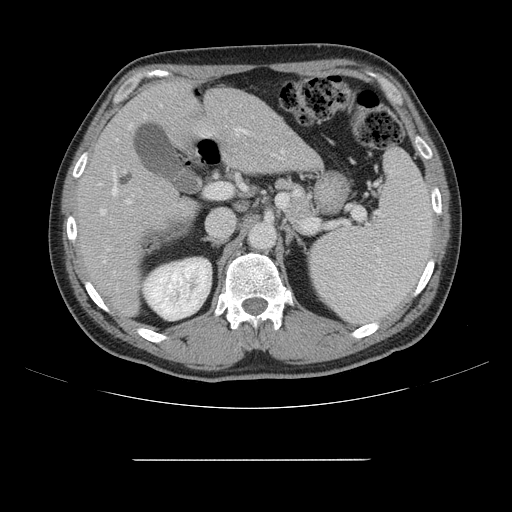
Contrast-enhanced abdominal CT, one axial slice. Slice 91 of 164 in the series (ordered by position). 120 kVp. Intravenous contrast given. Soft-tissue window (W 400 / L 40 HU). 2.5 mm slice thickness. 512 × 512 image matrix, field of view 404 × 404 mm. Male patient, age 54 years. From the clinical record (not read from this slice): diagnosis: colorectal cancer liver metastases, imaged before liver resection; multiple liver metastases: yes; largest metastasis: 1 cm; disease in both lobes: no.
Annotated regions visible in this slice (outlined manually by an expert reader):
- hepatic veins: bounding box <100,149,284,263> (left, top, right, bottom; pixels)
- liver: <79,81,318,315>
- planned liver remnant (the part of the liver to remain after resection): <79,81,231,315>
- portal vein (with intrahepatic branches): <126,114,249,204>